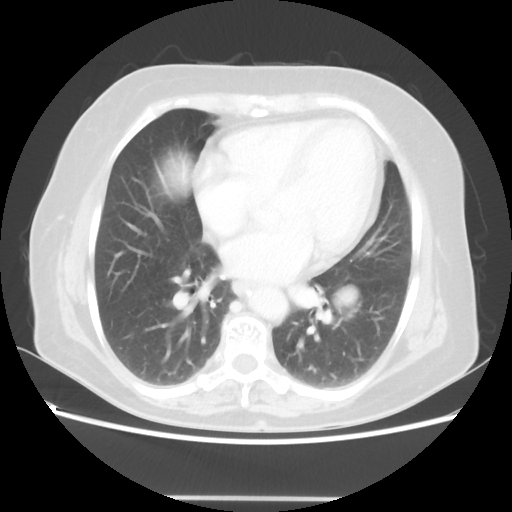
Chest CT, one axial slice; slice 25 of 56 in the series (ordered by position); 100 kVp; lung window (W 1500 / L -600 HU); 5 mm slice thickness; 512 × 512 image matrix, field of view 360 × 360 mm. Patient: female, 73 years. Case-level facts recorded for this patient, not image findings: clinical TNM (as recorded): T1c N0 M0.
Structures marked on this image (bounding box drawn by a radiologist):
- lung tumour (recorded histology: adenocarcinoma): bounding box <337,286,357,309> (left, top, right, bottom; pixels)